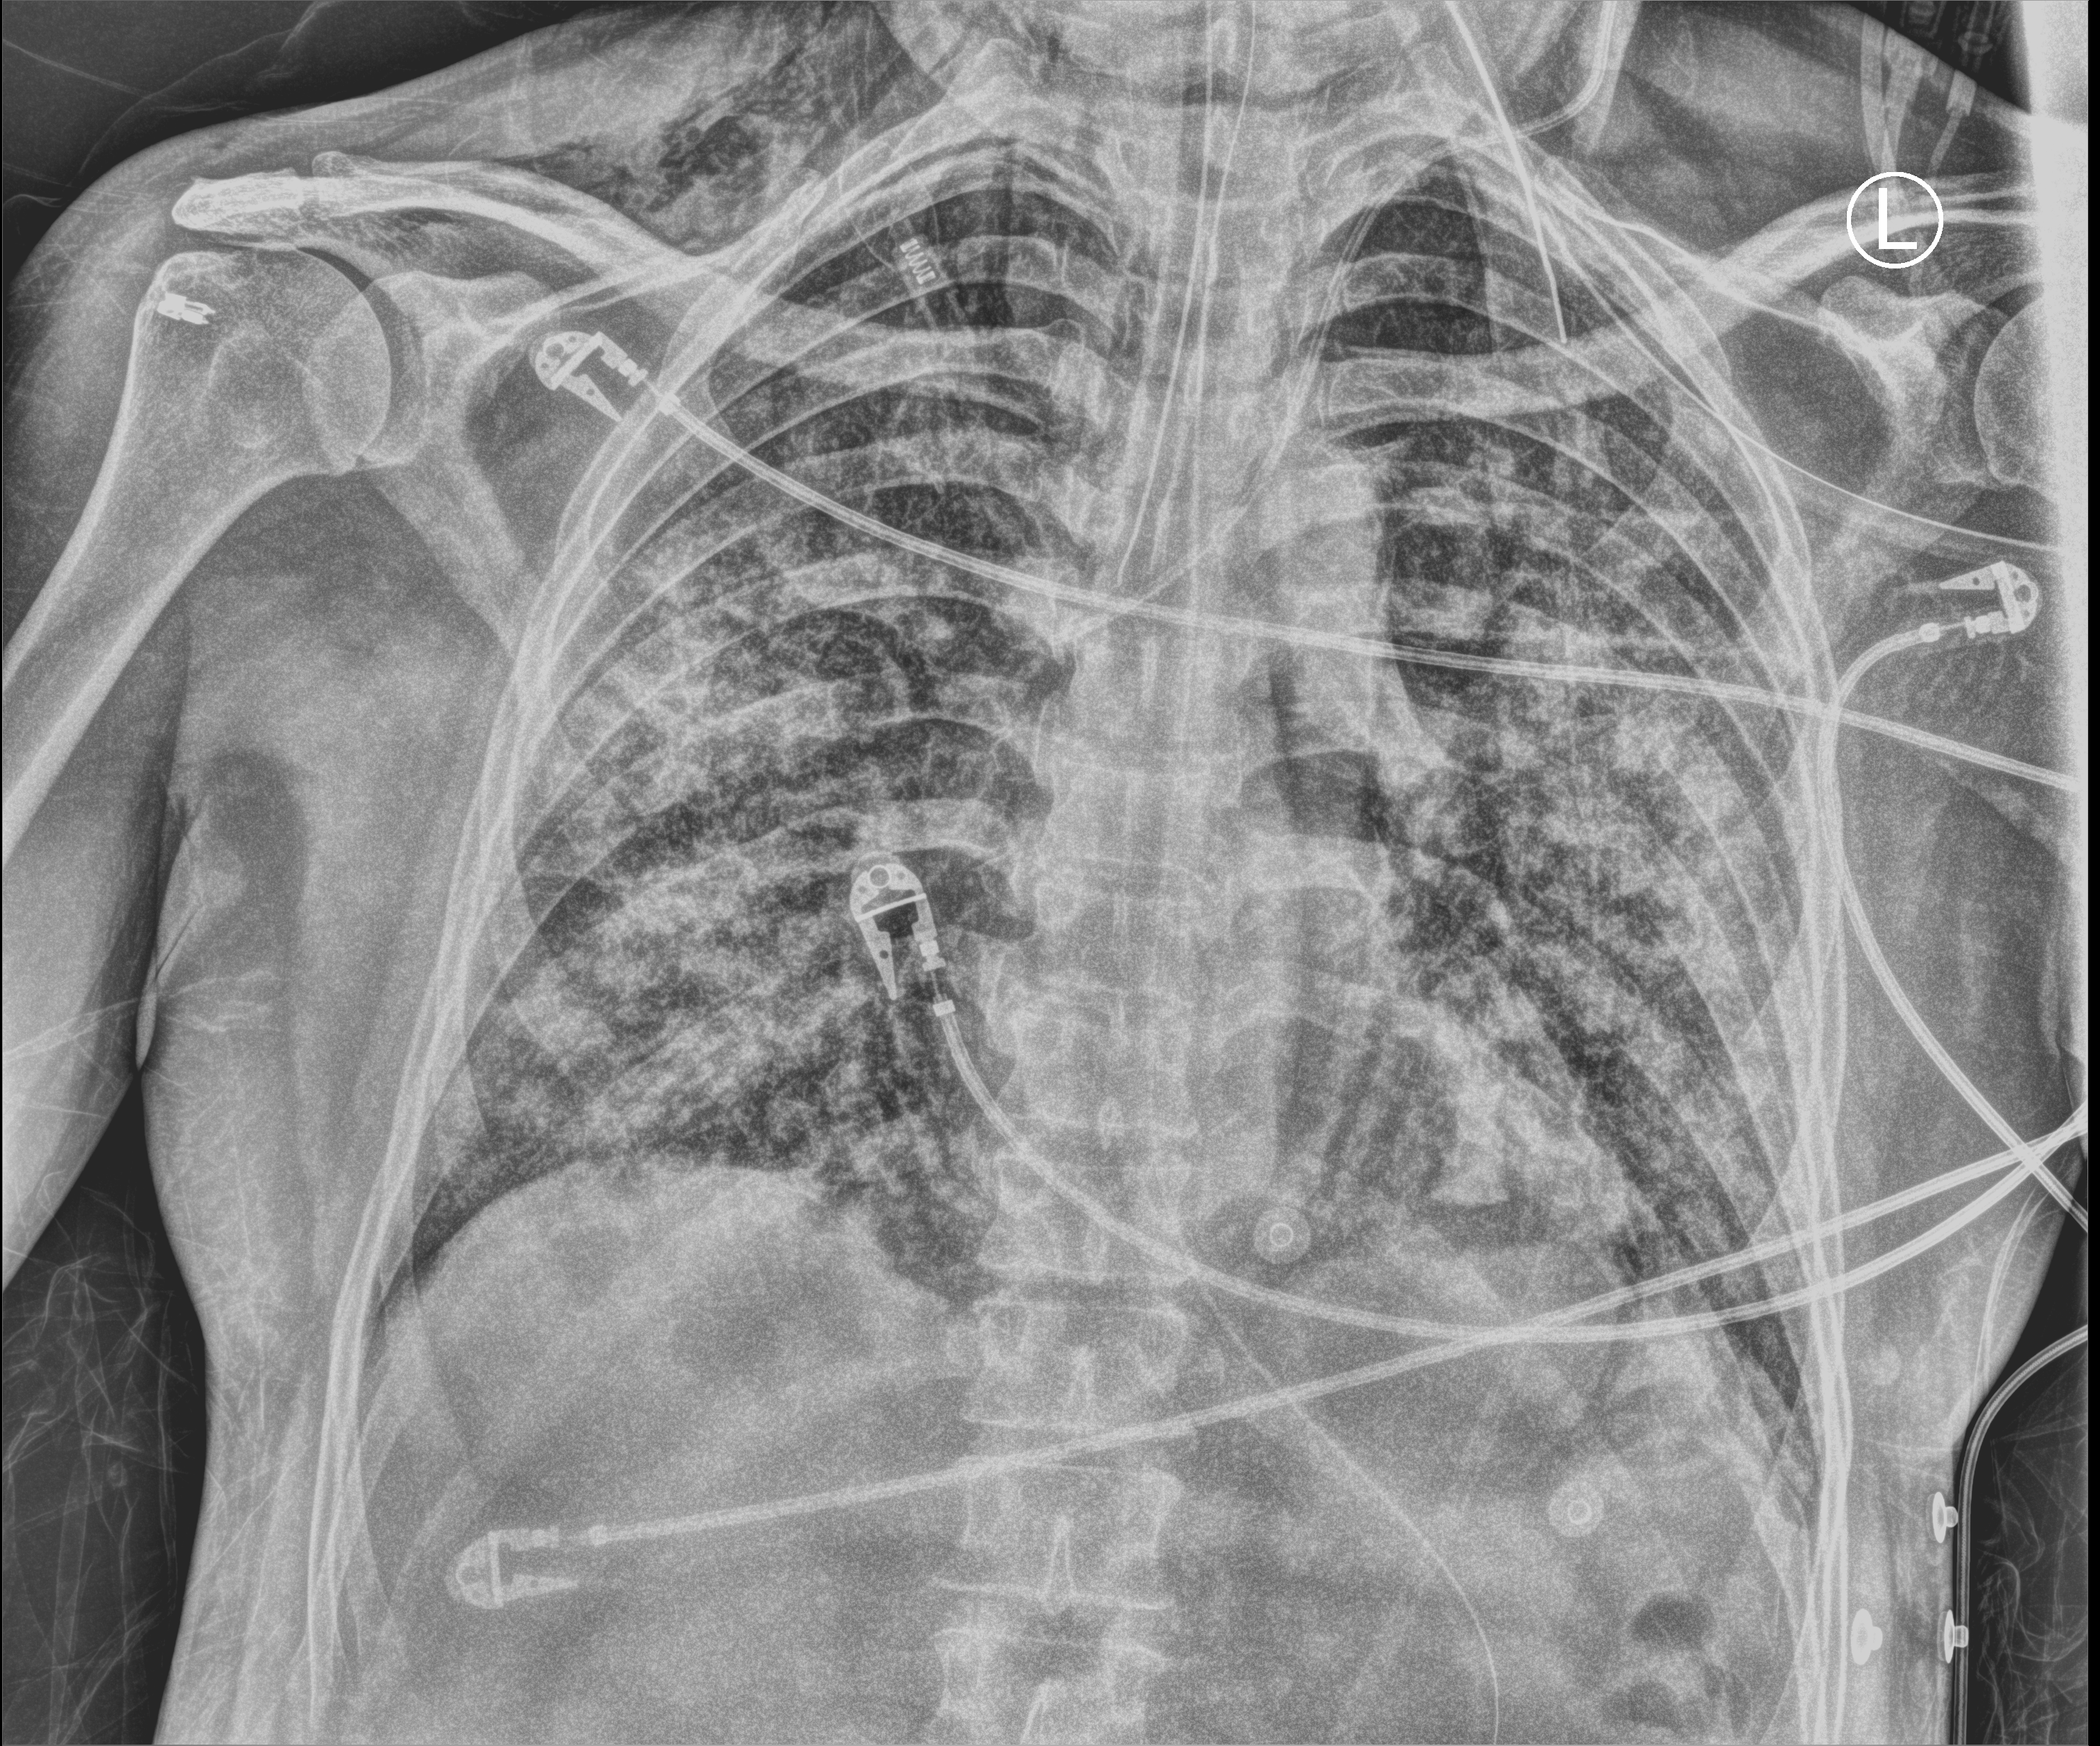
Bedside chest radiograph (computed radiography), anteroposterior (AP) projection. Patient hospitalised with COVID-19; male, aged 60–74 years.
From the hospital-stay record, not from the radiograph (when in the stay this image was taken is not recorded): mechanically ventilated during this hospital stay: yes.